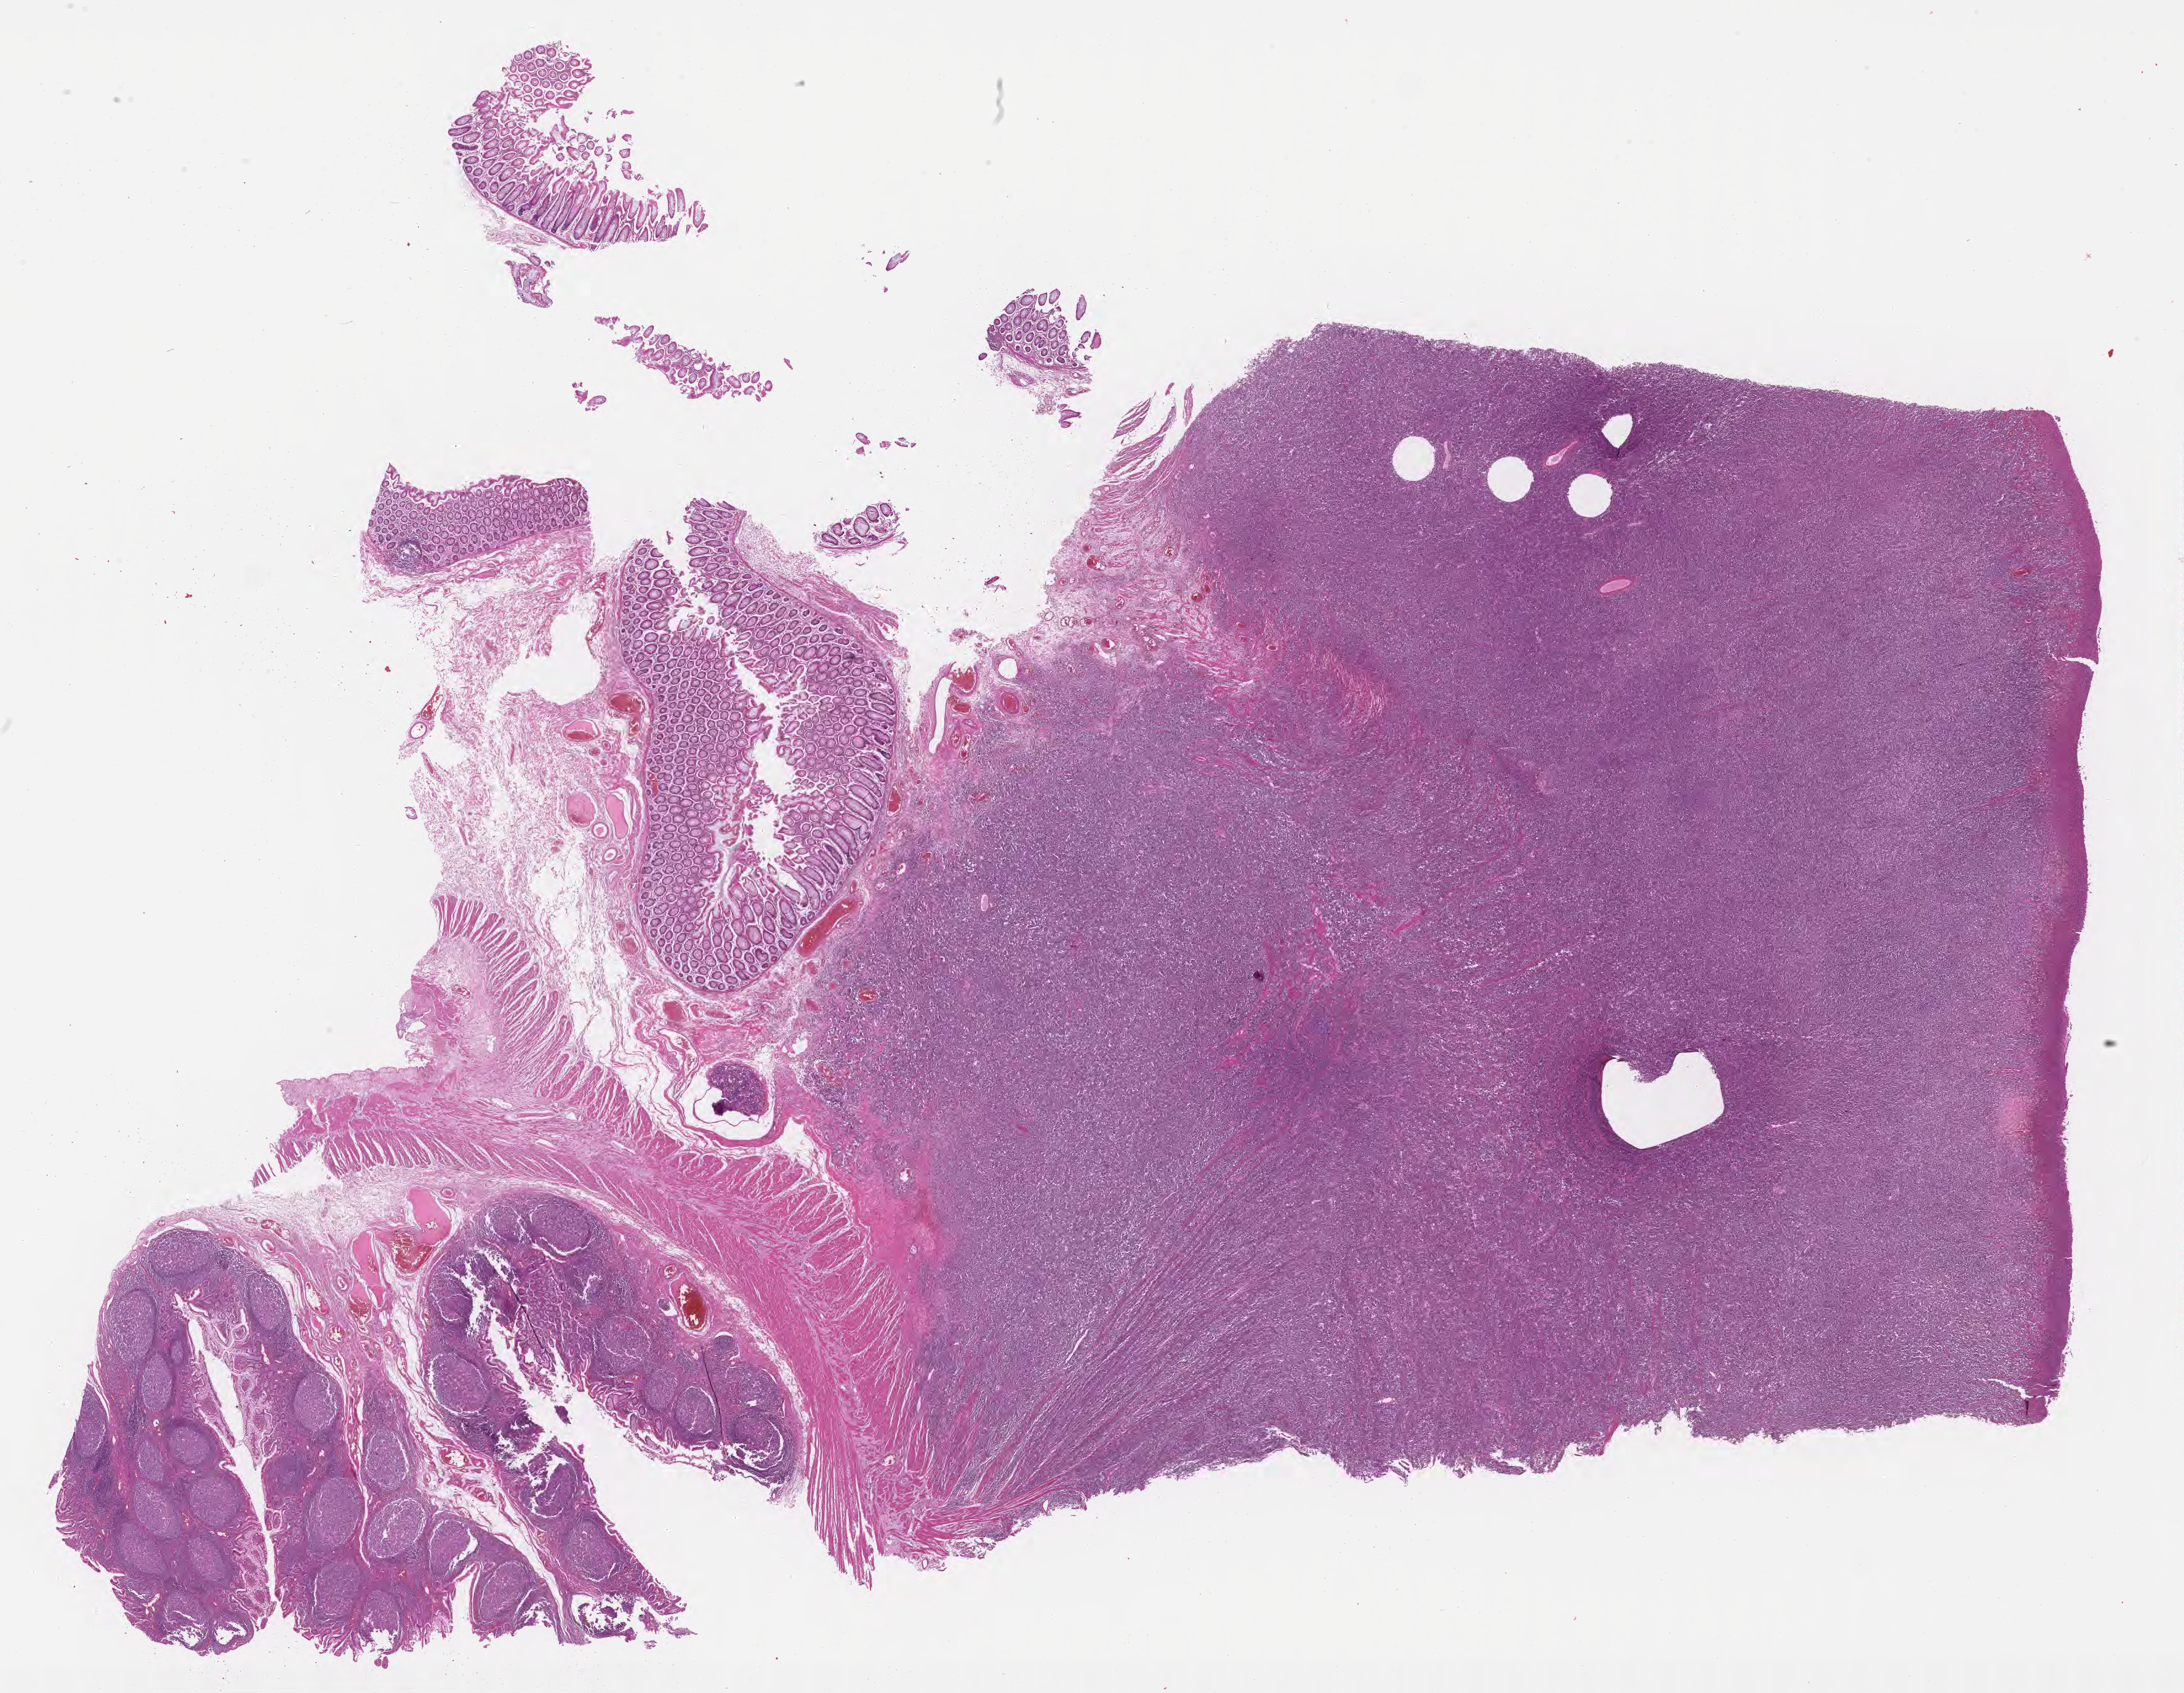
Digitized hematoxylin and eosin (H&E)-stained section, shown as a low-resolution overview of the whole scanned area (about 28.7 x 22.2 mm). Formalin-fixed paraffin-embedded section. Primary tumor. Male, age 7 years at initial diagnosis. Slide review estimates, as recorded: tumor cells 50%, tumor nuclei 75%, stromal cells 5%, necrosis 0%, normal cells 45%. Inflammatory infiltration, as recorded: lymphocyte infiltration 90%, monocyte infiltration 5%, neutrophil infiltration 0%.
Section: bottom of the tissue portion. Ann Arbor stage (patient): Stage II. Diagnosis: Burkitt lymphoma, NOS.